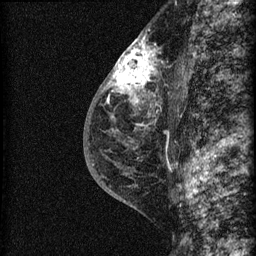
Breast MRI (dynamic contrast-enhanced), one sagittal slice; position 38 of 60 along the scan axis; dynamic contrast-enhanced series, image 2 of 3 at this slice position (ordered by acquisition); 1.5 T; TE 4.2 ms, TR 22.7 ms; 1.5 mm slice thickness; 256 × 256 image matrix, field of view 180 × 180 mm. Female patient, age 48 years. Case-level facts recorded for this patient, not image findings: setting: breast cancer imaged before/during neoadjuvant chemotherapy; receptor status: triple-negative.
Structures marked on this image (semi-automatic segmentation, software-assisted and operator-edited):
- analysis volume of interest (the breast-tissue region the enhancement analysis was run in; not a lesion): bounding box [x1, y1, x2, y2] px = [115, 34, 169, 162]
- tumour enhancement mask (voxels above the 90 % enhancement threshold inside the analysis volume of interest): [115, 35, 156, 104]